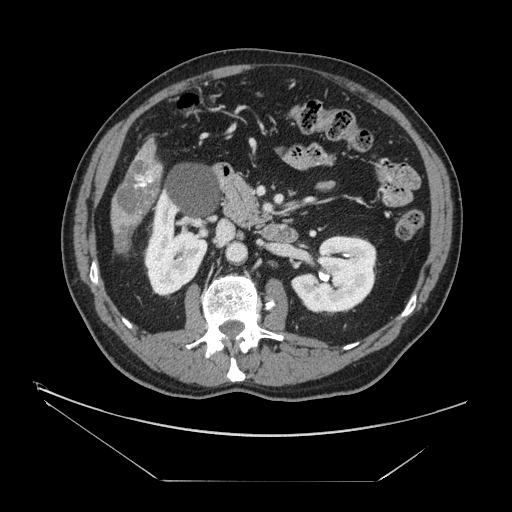
Contrast-enhanced abdominal CT, one axial slice; position 56 of 161 along the scan axis; reconstruction kernel STANDARD; intravenous contrast given; soft-tissue window (W 400 / L 40 HU); 2.5 mm slice thickness; 512 × 512 image matrix, field of view 440 × 440 mm. Male patient, age 65 years. Case-level facts recorded for this patient, not image findings: diagnosis: colorectal cancer liver metastases, imaged before liver resection; multiple liver metastases: yes; largest metastasis: 4.2 cm; chemotherapy before resection: yes.
Outlined on this slice (outlined manually by an expert reader):
- liver: box from (x=112, y=142) to (x=161, y=234) px
- portal vein (with intrahepatic branches): (x=136, y=169)–(x=154, y=187)
- liver metastasis: (x=115, y=230)–(x=130, y=251)
- liver metastasis: (x=116, y=160)–(x=160, y=217)